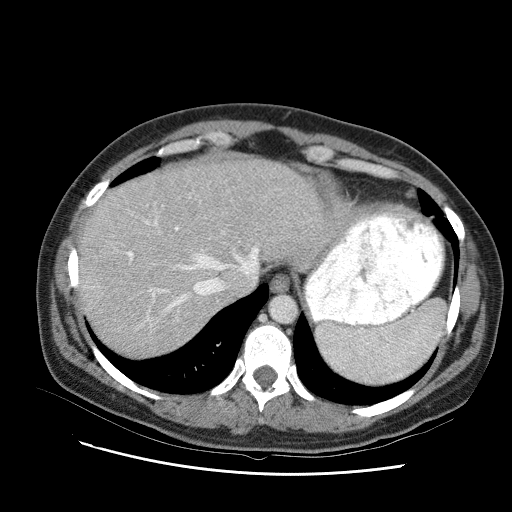
Contrast-enhanced abdominal CT (liver protocol), one axial slice. Slice 77 of 95 in the series (ordered by position). Reconstruction kernel STANDARD. 120 kVp. One of 2 acquisitions stored at this slice position. Soft-tissue window (W 400 / L 40 HU). 2.5 mm slice thickness. 512 × 512 image matrix. Case-level facts recorded for this patient, not image findings: diagnosis: hepatocellular carcinoma (patient treated with transarterial chemoembolisation; whether this scan precedes or follows treatment is not stated here); TNM stage (as recorded): Stage-I; Child-Pugh class: B; tumour differentiation: moderately differentiated.
Annotated regions visible in this slice (semi-automatic segmentation, software-assisted and operator-edited):
- liver parenchyma outside the tumour (the mass and vessels are separate outlines, so this box may not span the whole liver): bounding box <78,150,310,336> (left, top, right, bottom; pixels)
- liver vessels: <102,227,221,292>